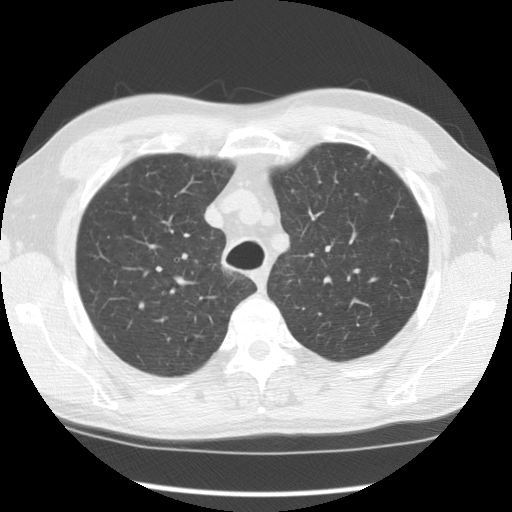
Low-dose screening chest CT, one axial slice. Position 95 of 121 along the scan axis. 120 kVp. Lung window (W 1500 / L -600 HU). 2.5 mm slice thickness. 512 × 512 image matrix.
Annotated regions visible in this slice (outlined manually by an expert reader):
- lesion 1 (tumor, upper lobe of left lung): bounding box [x1, y1, x2, y2] px = [367, 153, 373, 159]